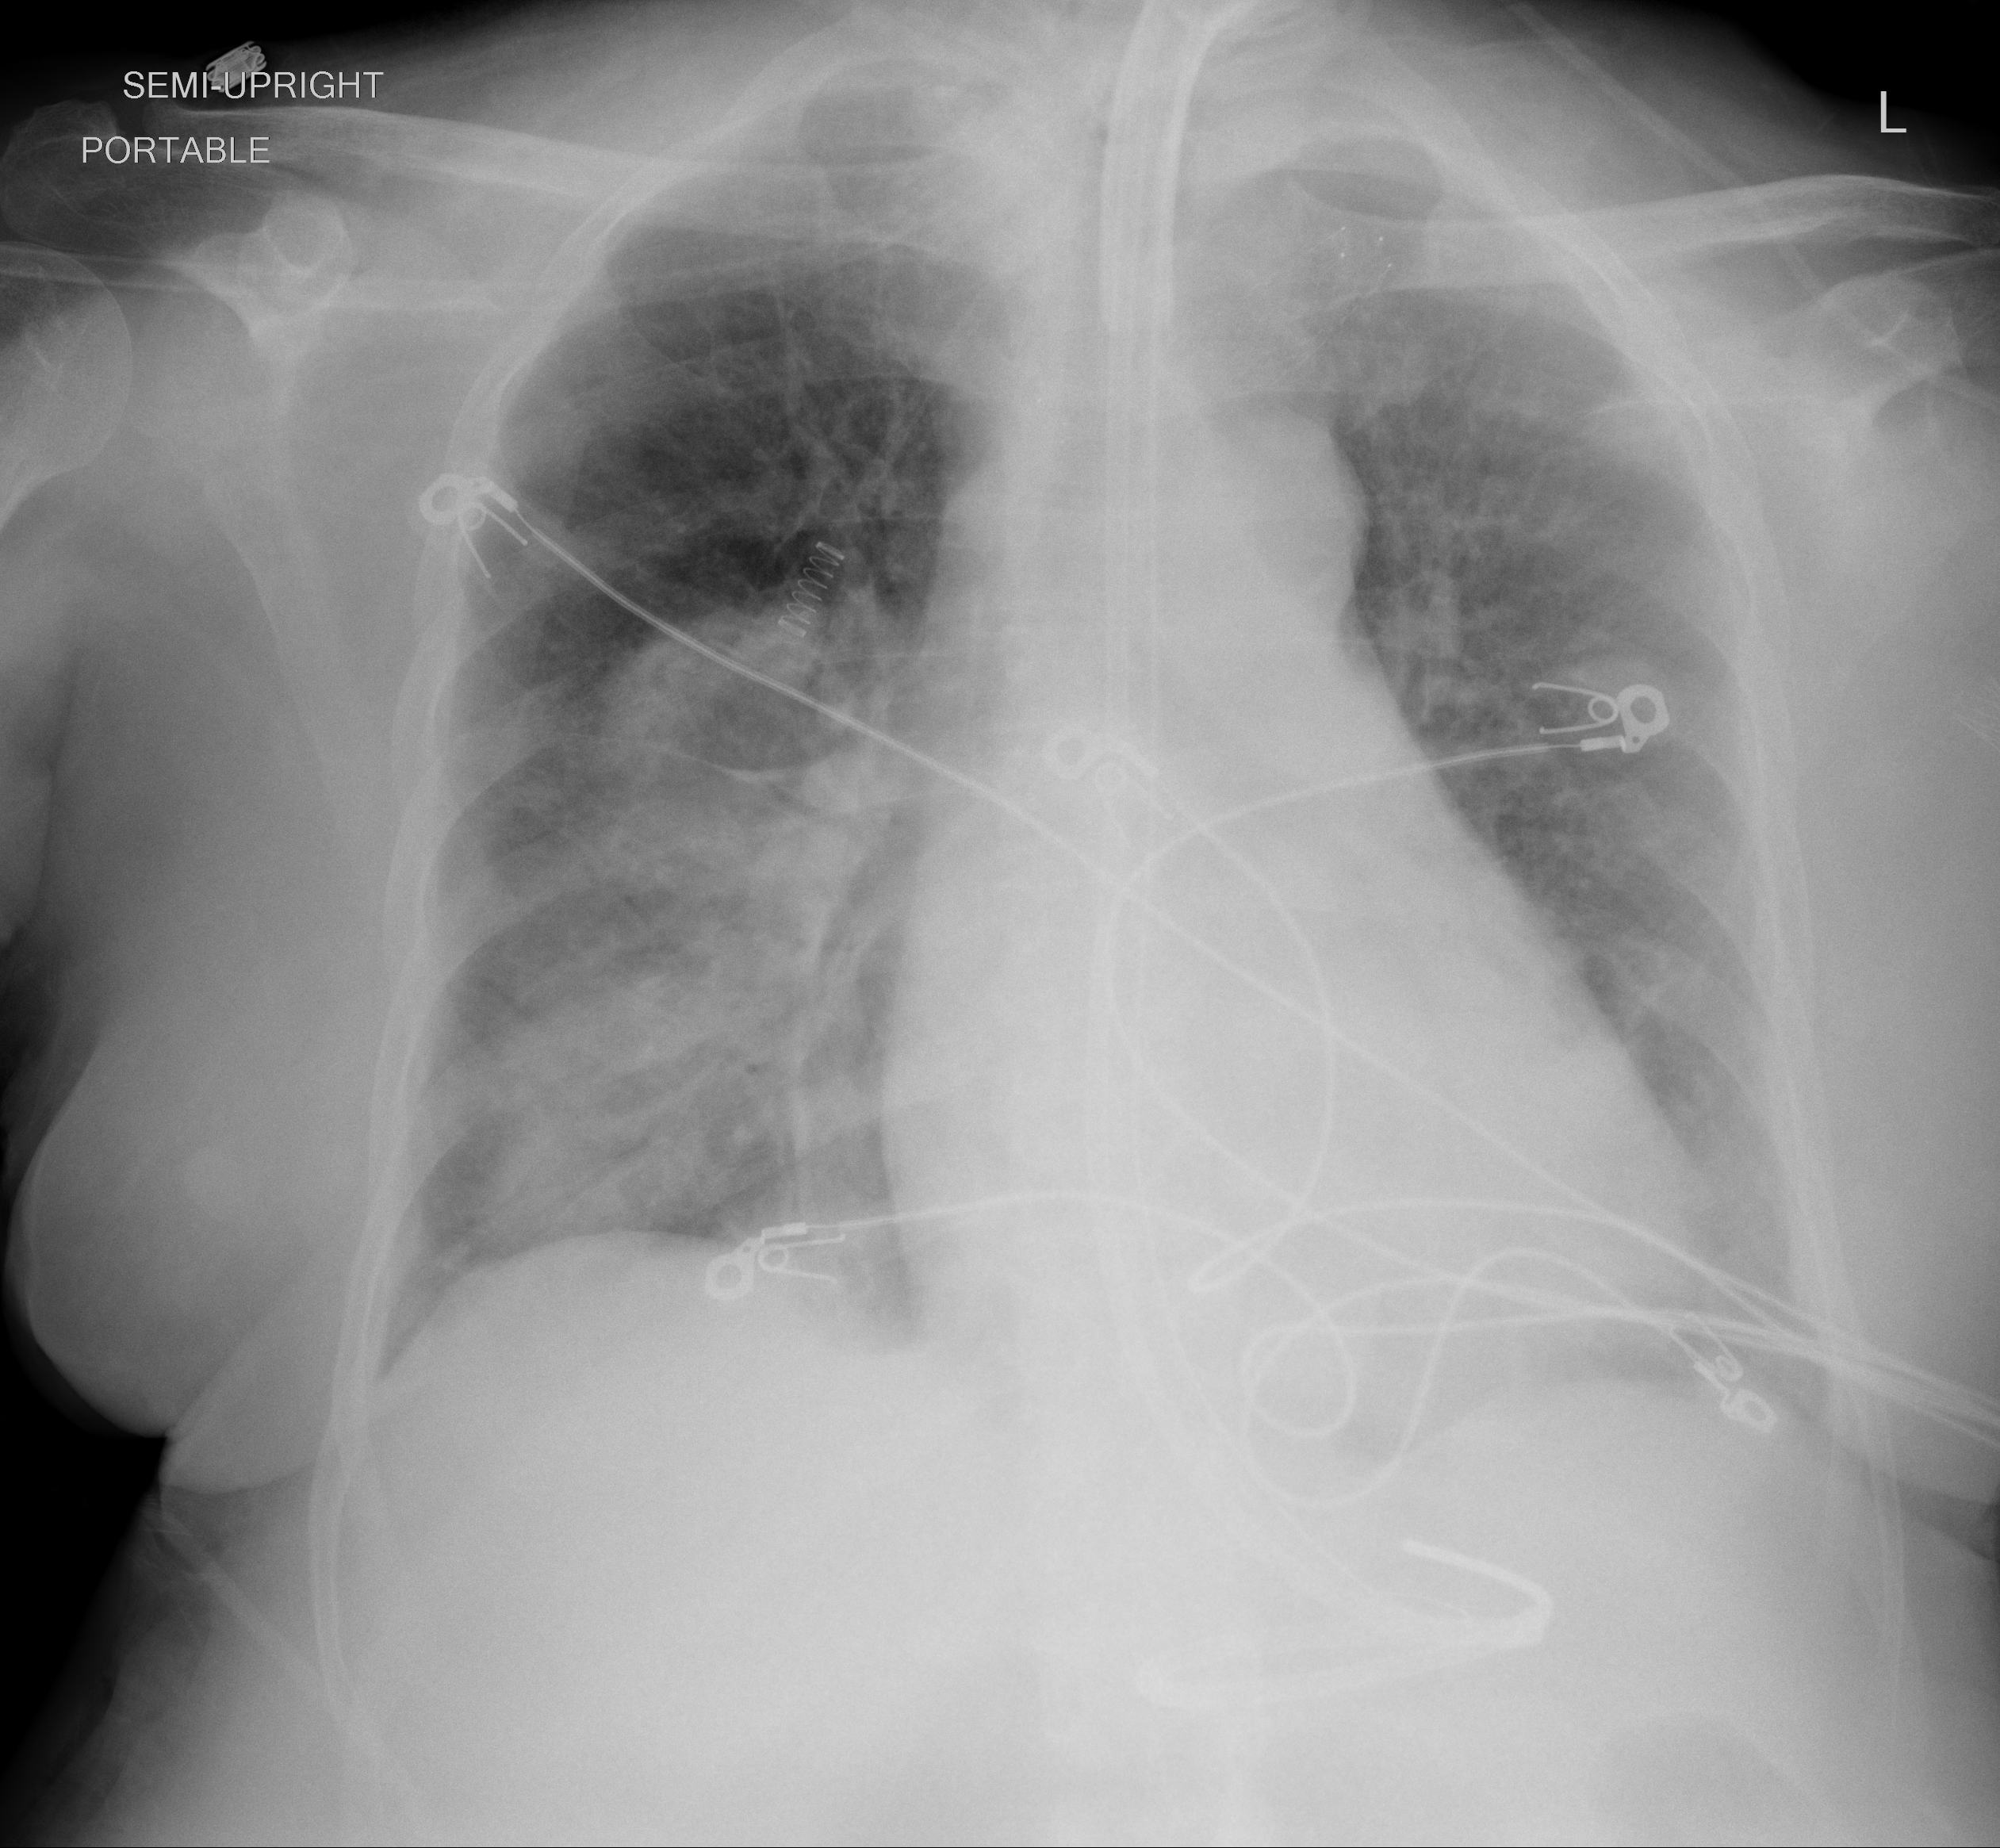
Portable chest radiograph, AP projection. Female patient, age 64 years; COVID-19 (test-positive).
Key findings recorded by the radiologist: Ill-defined airspace disease continuing in the lung bases mainly in the lower lobes and in the right perihilar region. These airspace opacities have worsened slightly in the interval.